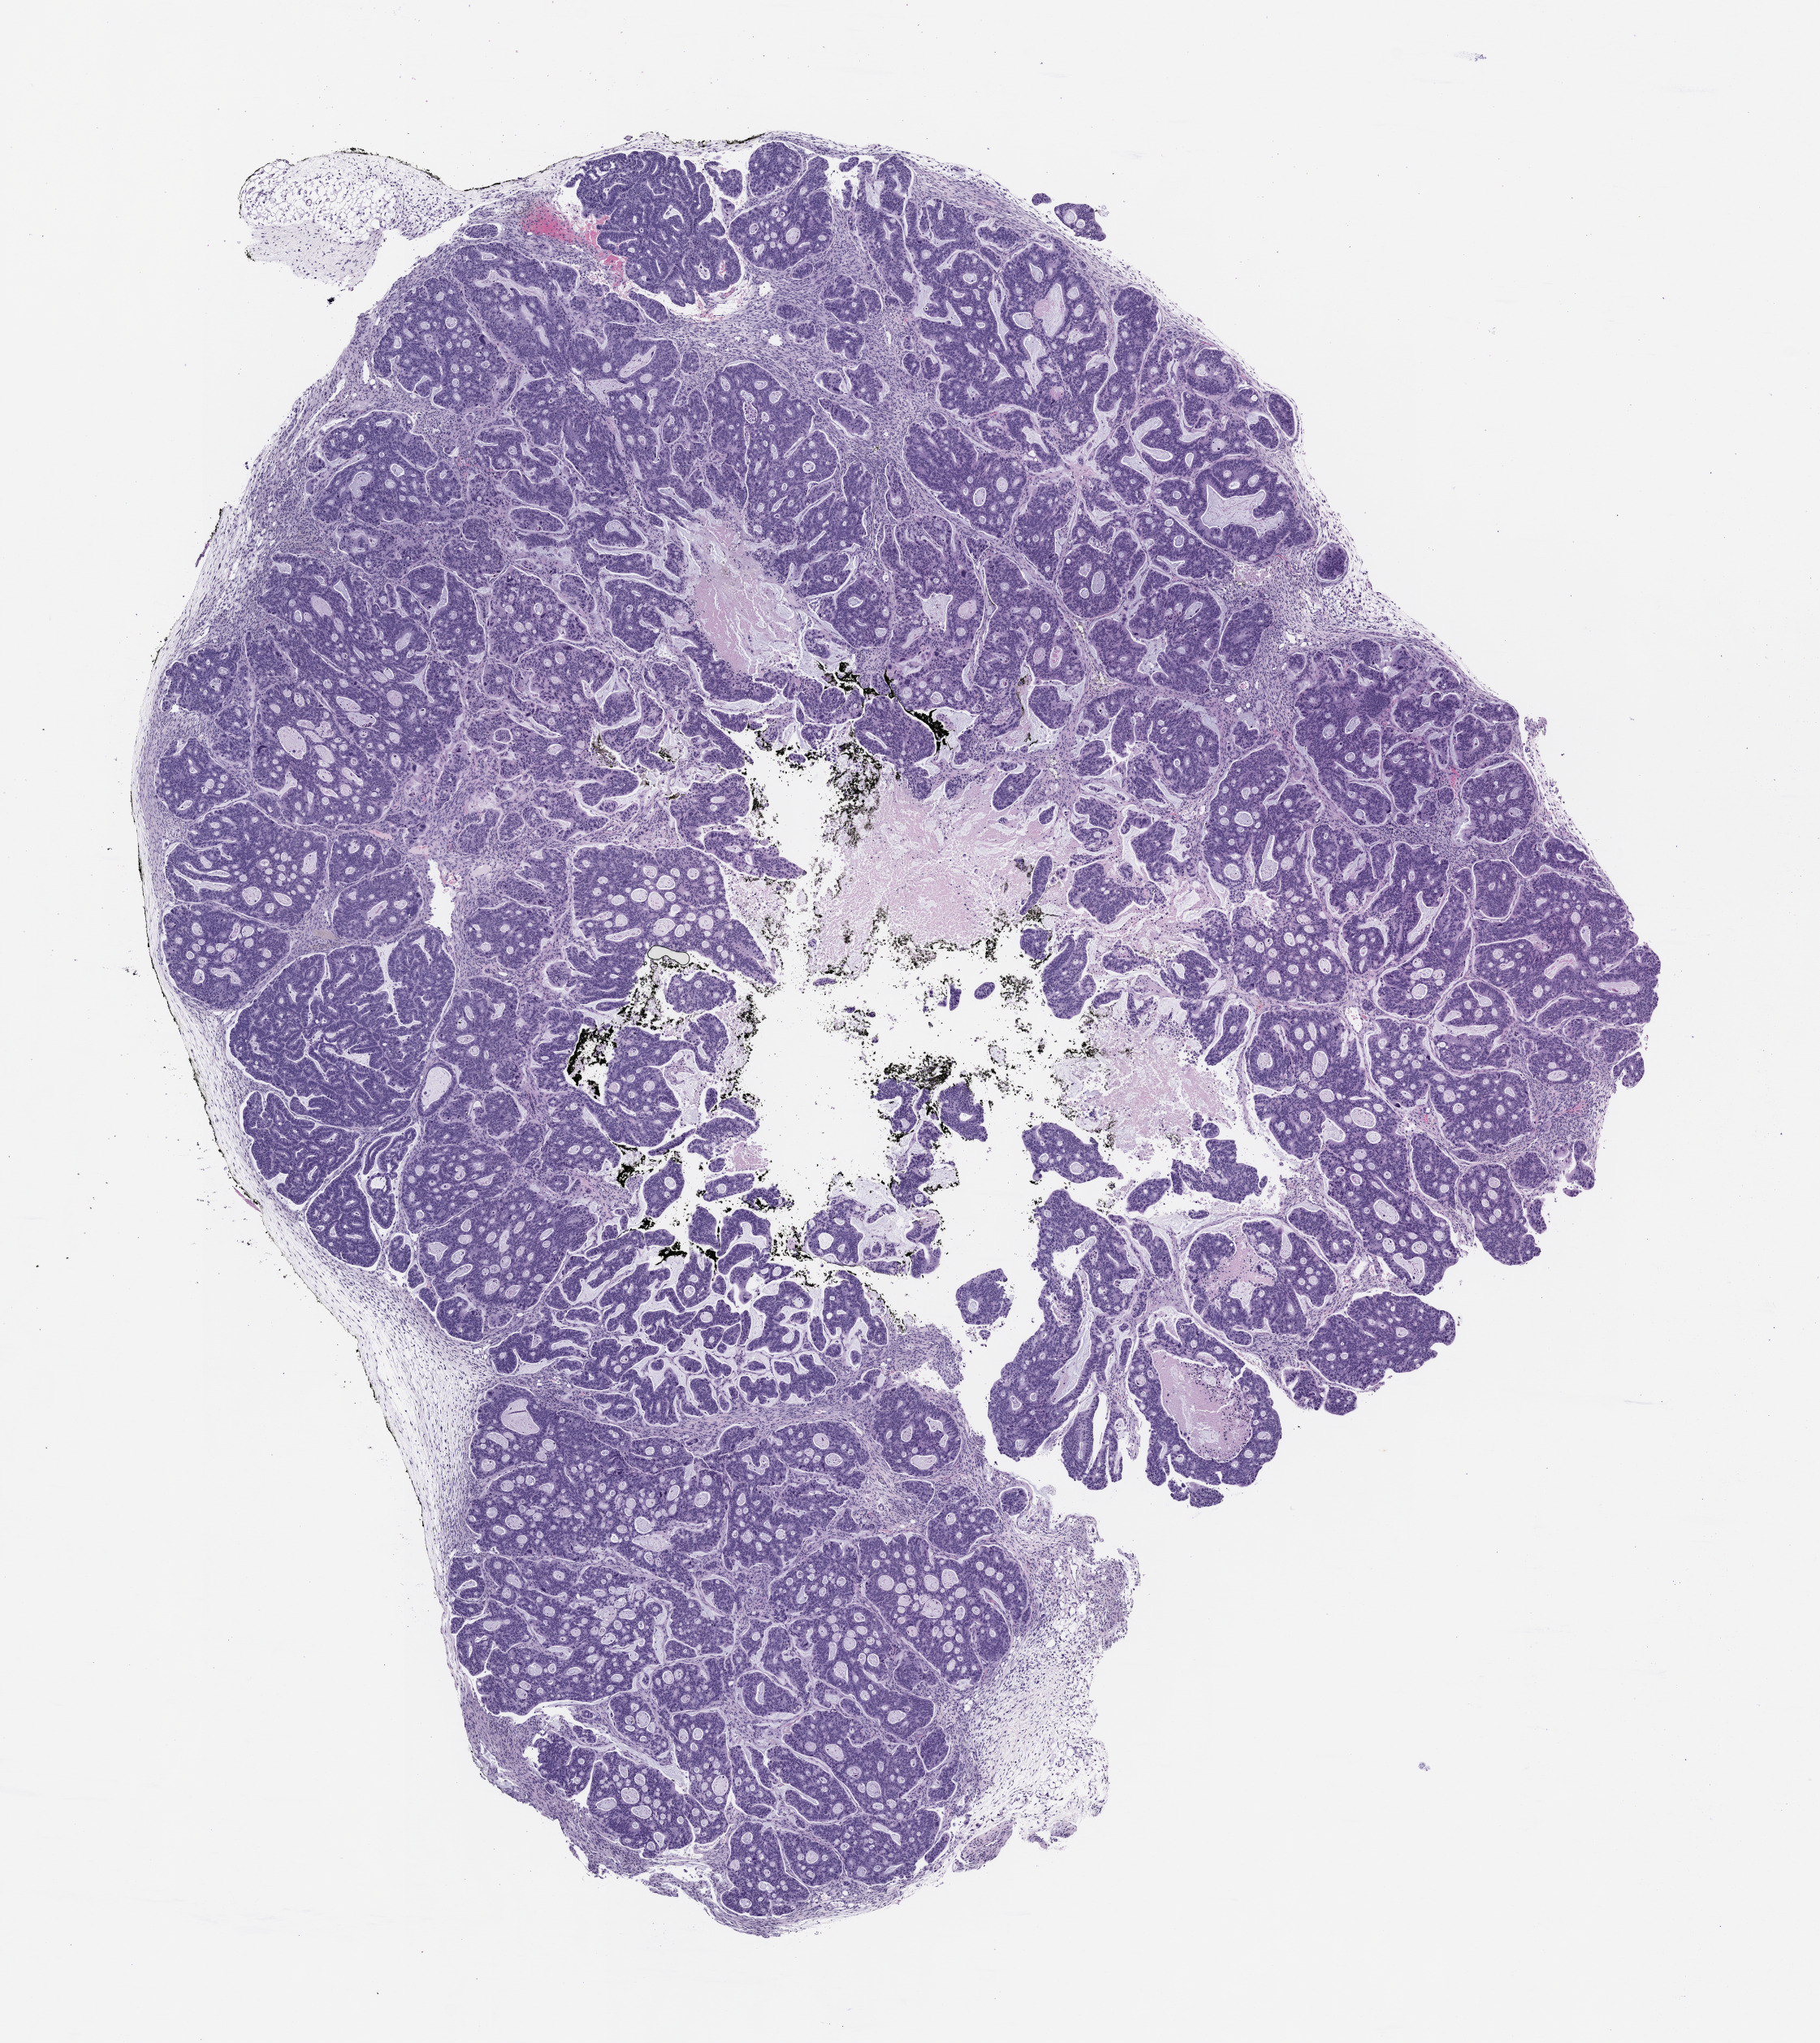
Haematoxylin and eosin whole-slide image of a patient-derived xenograft (PDX) tumor grown in a mouse, passage 1 — low-resolution overview of the scanned area, about 9.0 x 10.1 mm; FFPE section; tumor site category: colon.
Originating patient diagnosis: Colon Adenocarcinoma.